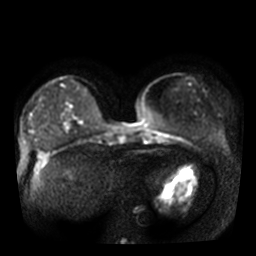
Breast MRI, one axial slice; slice 11 of 36 in the series (ordered by position); diffusion-weighted series; image 2 of 4 stored at this slice position (different b-values; order by instance number); 3 T; 5 mm slice thickness; 256 × 256 image matrix, field of view 340 × 340 mm. Female patient.
Structures marked on this image (manually delineated by an expert):
- tumour on diffusion-weighted imaging: box from (x=68, y=123) to (x=71, y=128) px